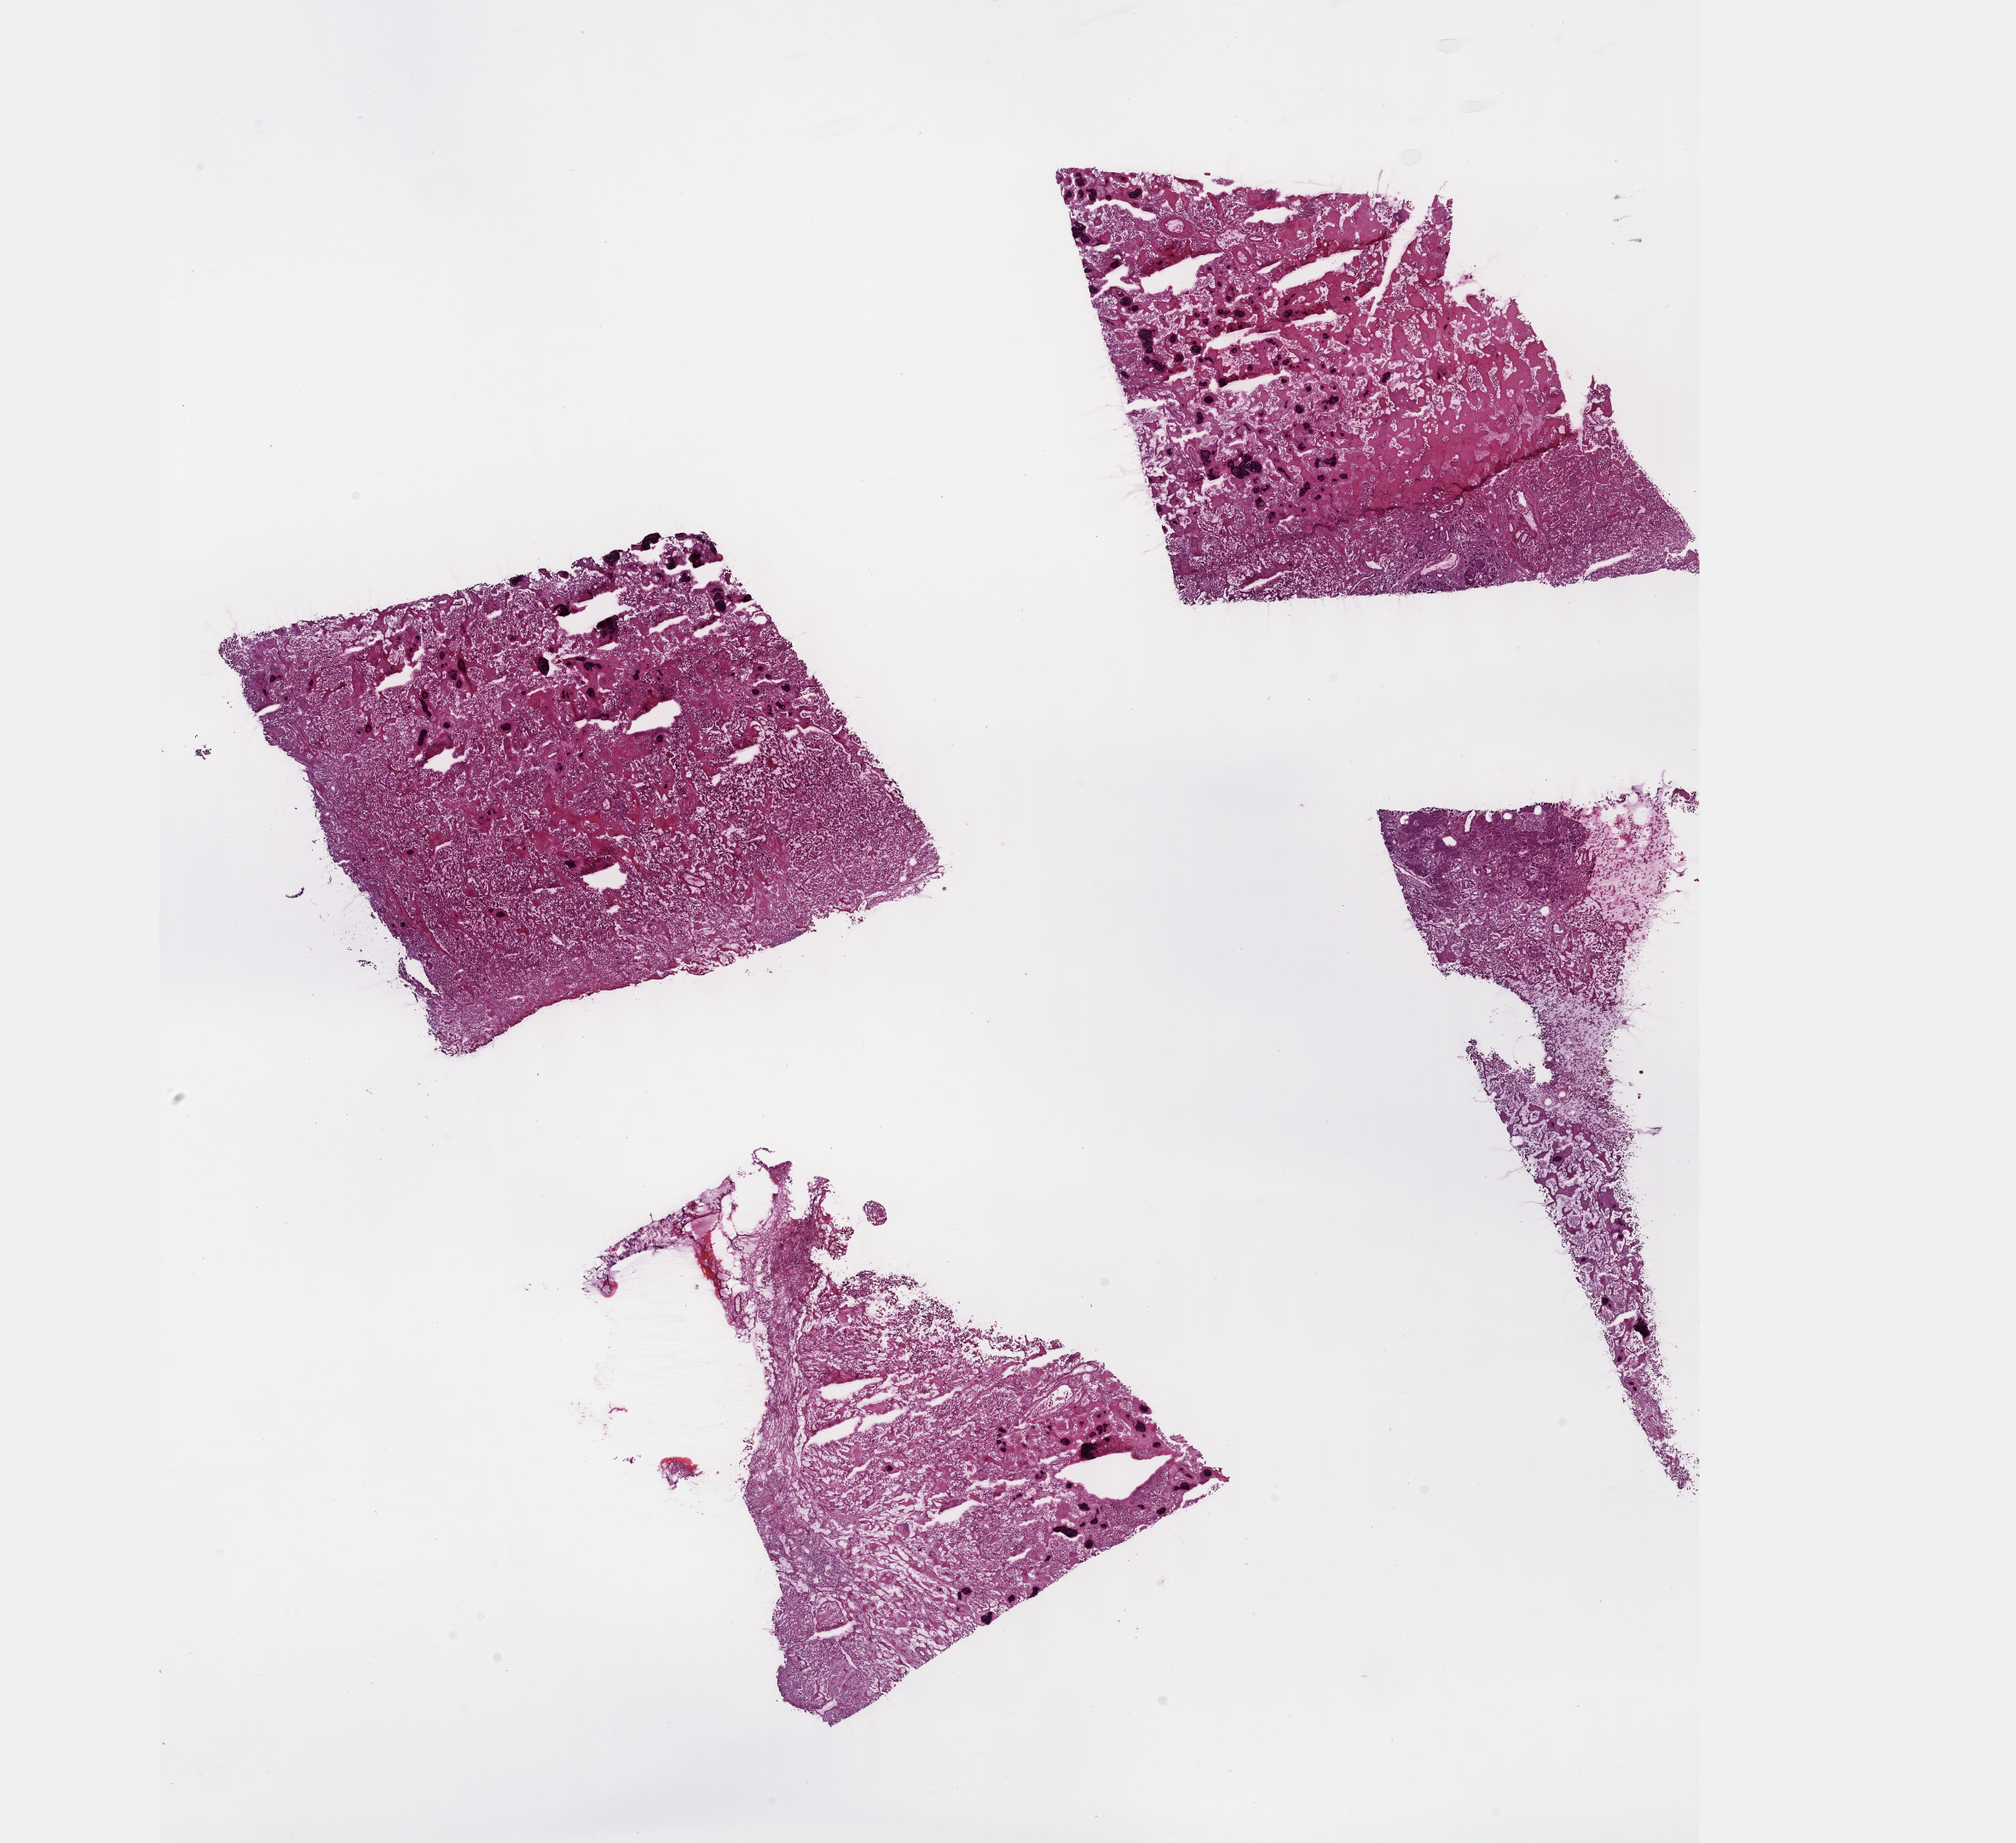
H&E whole-slide image, whole scanned area (about 19.1 x 17.5 mm, acquisition: 40x scan) shown as a low-resolution overview; frozen section; pancreas, primary tumour sample. Male patient; age at initial diagnosis 55 years. Histologic grade: G1 (well differentiated). Composition of this section per pathologist review: tumour cells 70%, tumour nuclei 70%, normal cells 5%, stromal cells 22%, necrosis 3%. Infiltration values recorded for this section: lymphocyte infiltration 2%, monocyte infiltration 1%, neutrophil infiltration 3%.
• pathologic diagnosis: Neuroendocrine carcinoma, NOS (body of pancreas)